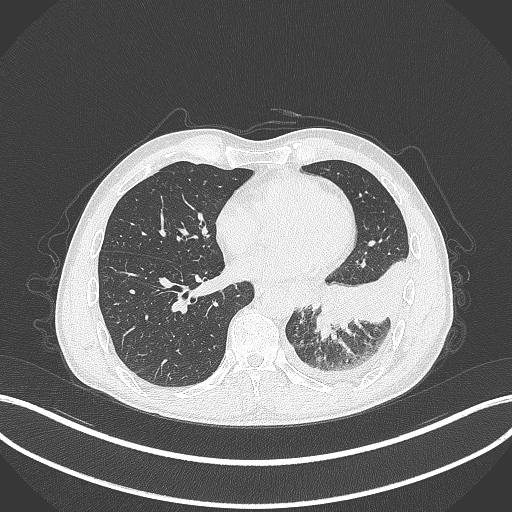
Chest CT, one axial slice; position 114 of 295 along the scan axis; reconstruction kernel B70f; lung window (W 1500 / L -600 HU); 1 mm slice thickness; 512 × 512 image matrix. Male patient, age 47 years. From the clinical record (not read from this slice): clinical TNM (as recorded): T3 N1 M1c.
Outlined on this slice (rectangle marked by the reading radiologist):
- lung tumour (recorded histology: small cell carcinoma): box from (x=310, y=308) to (x=336, y=342) px